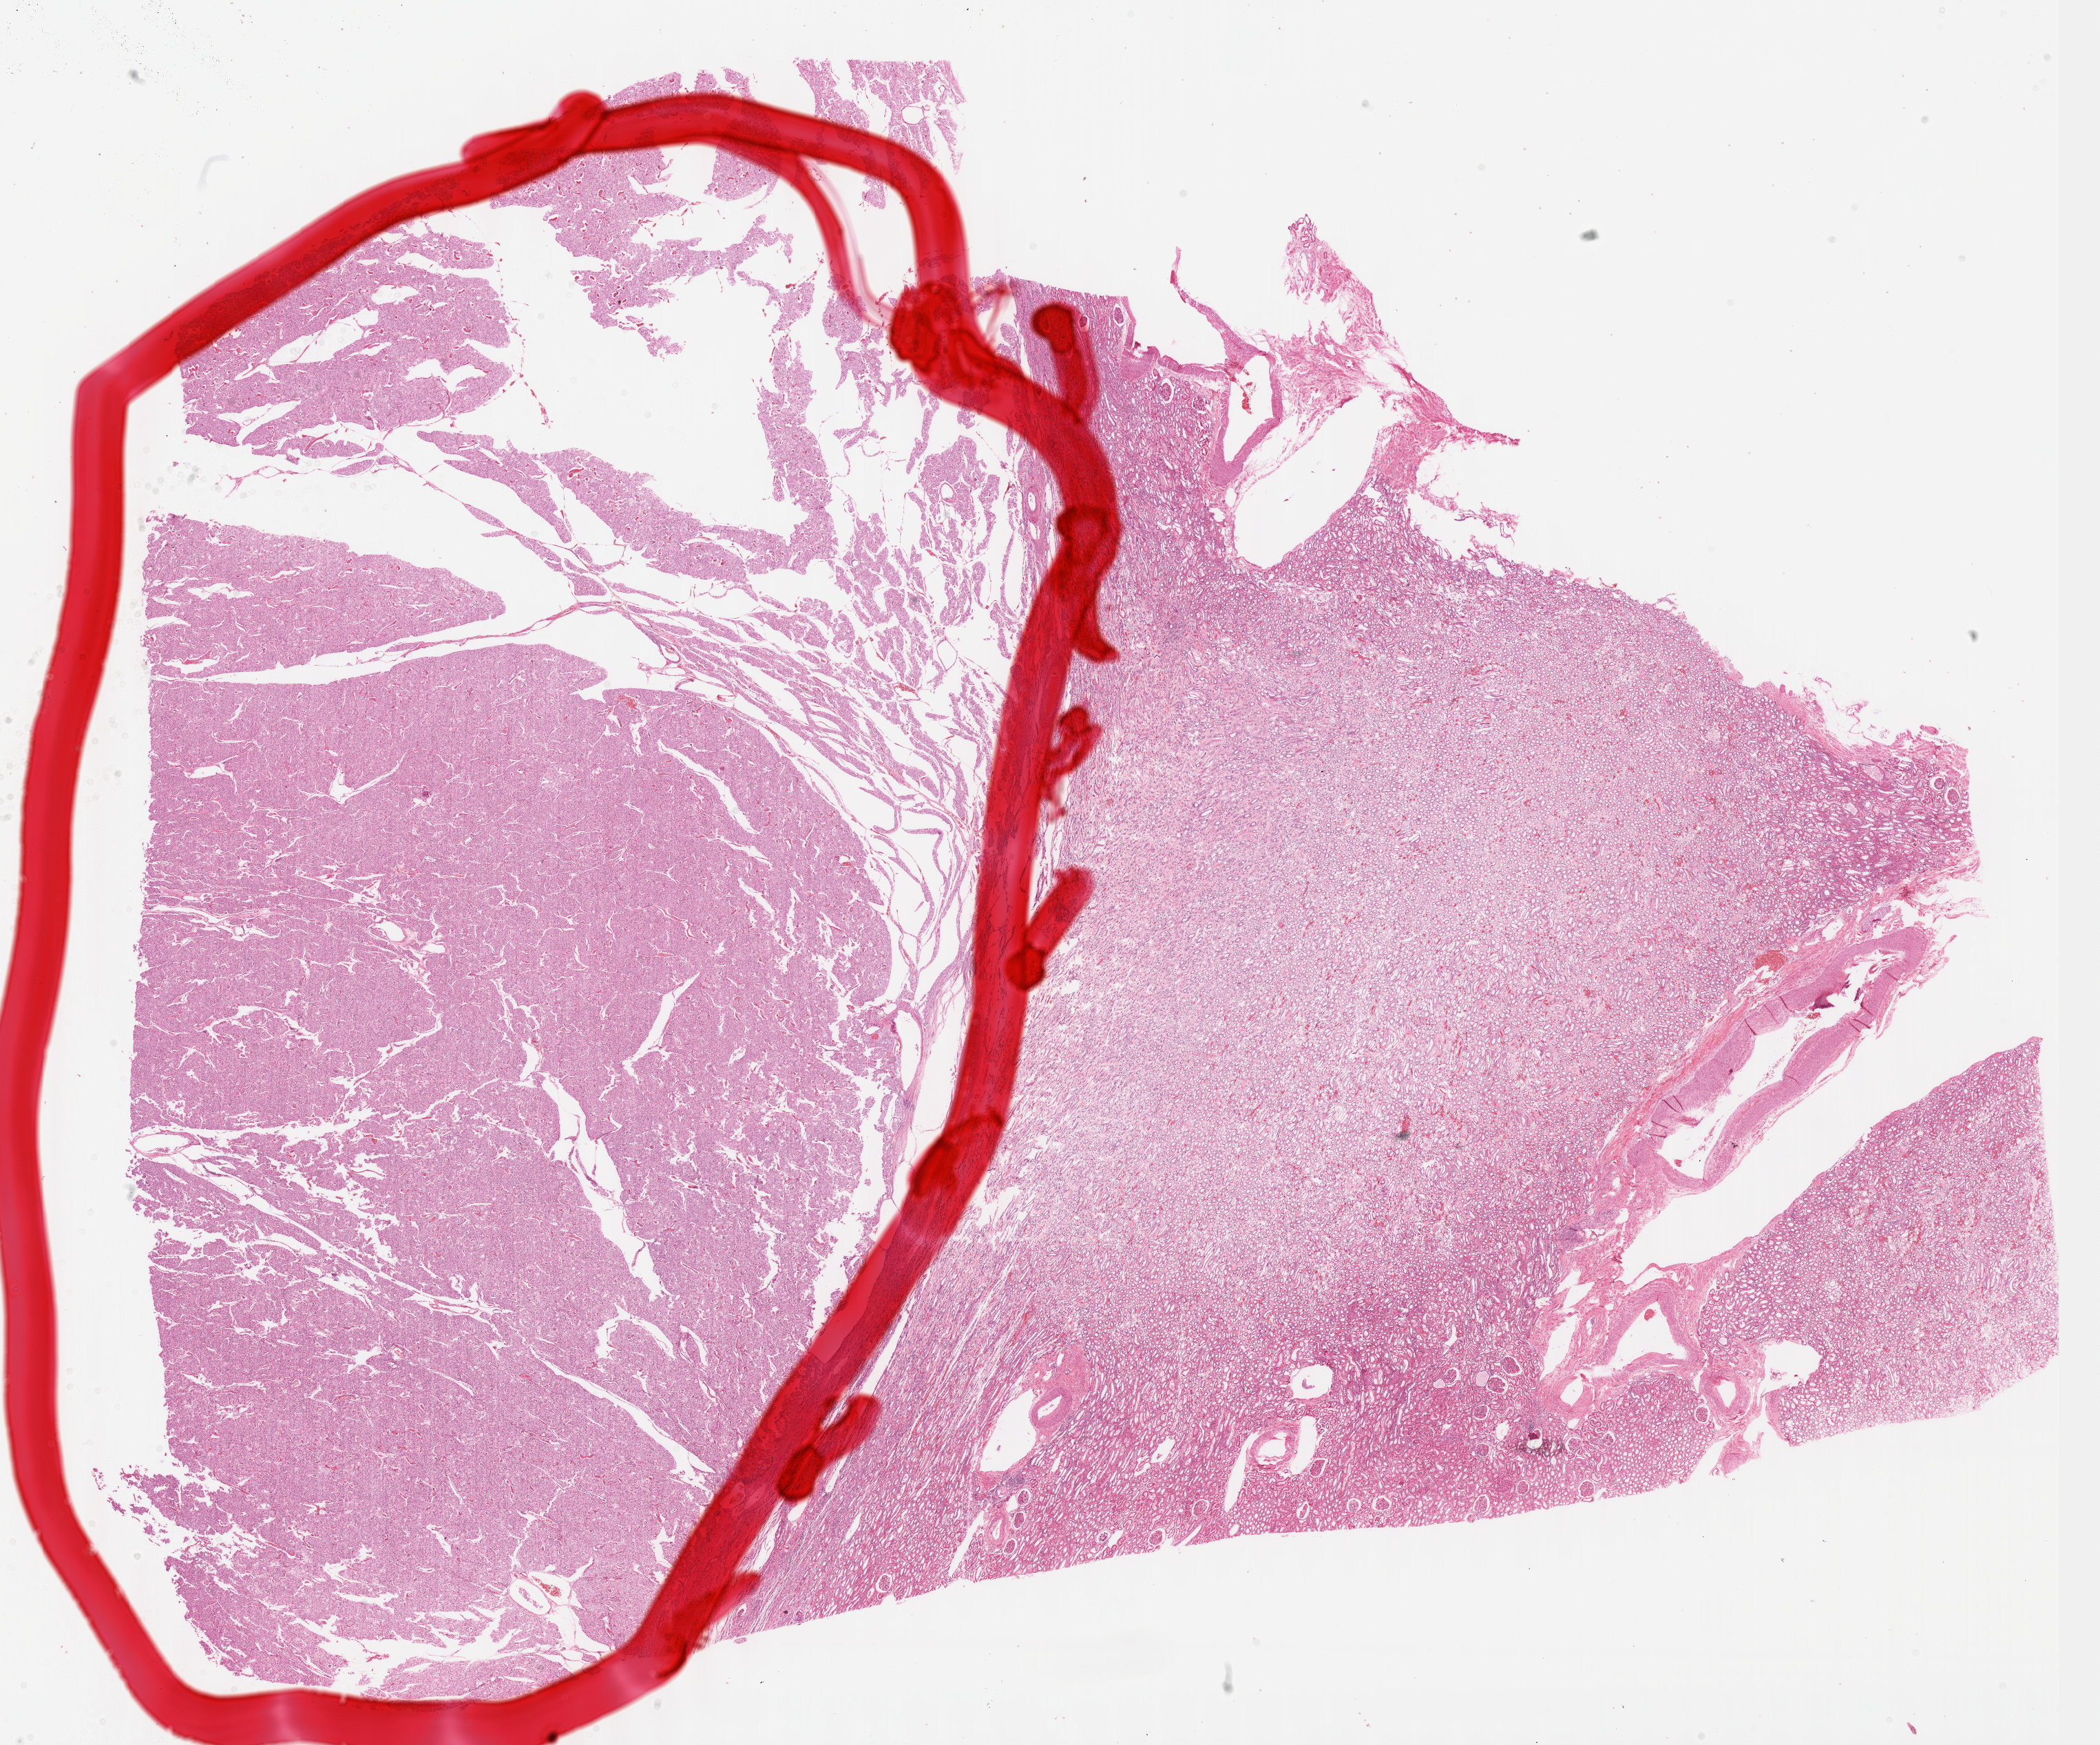
H&E whole-slide image, a low-resolution overview of the entire scanned area, about 24.6 x 20.5 mm (slide scanned at 40x), formalin-fixed paraffin-embedded (FFPE) diagnostic section, sample: primary tumour, kidney. Male, age 67 years at initial diagnosis. Slide review estimates, as recorded: tumour cells 96%, tumour nuclei 97%, normal cells 0%, stromal cells 4%, necrosis 0%. Inflammatory infiltration, as recorded: lymphocyte infiltration 1%, monocyte infiltration 0%, neutrophil infiltration 0%.
AJCC pathologic stage: I (6th edition). Pathologic diagnosis: Renal cell carcinoma, chromophobe type.